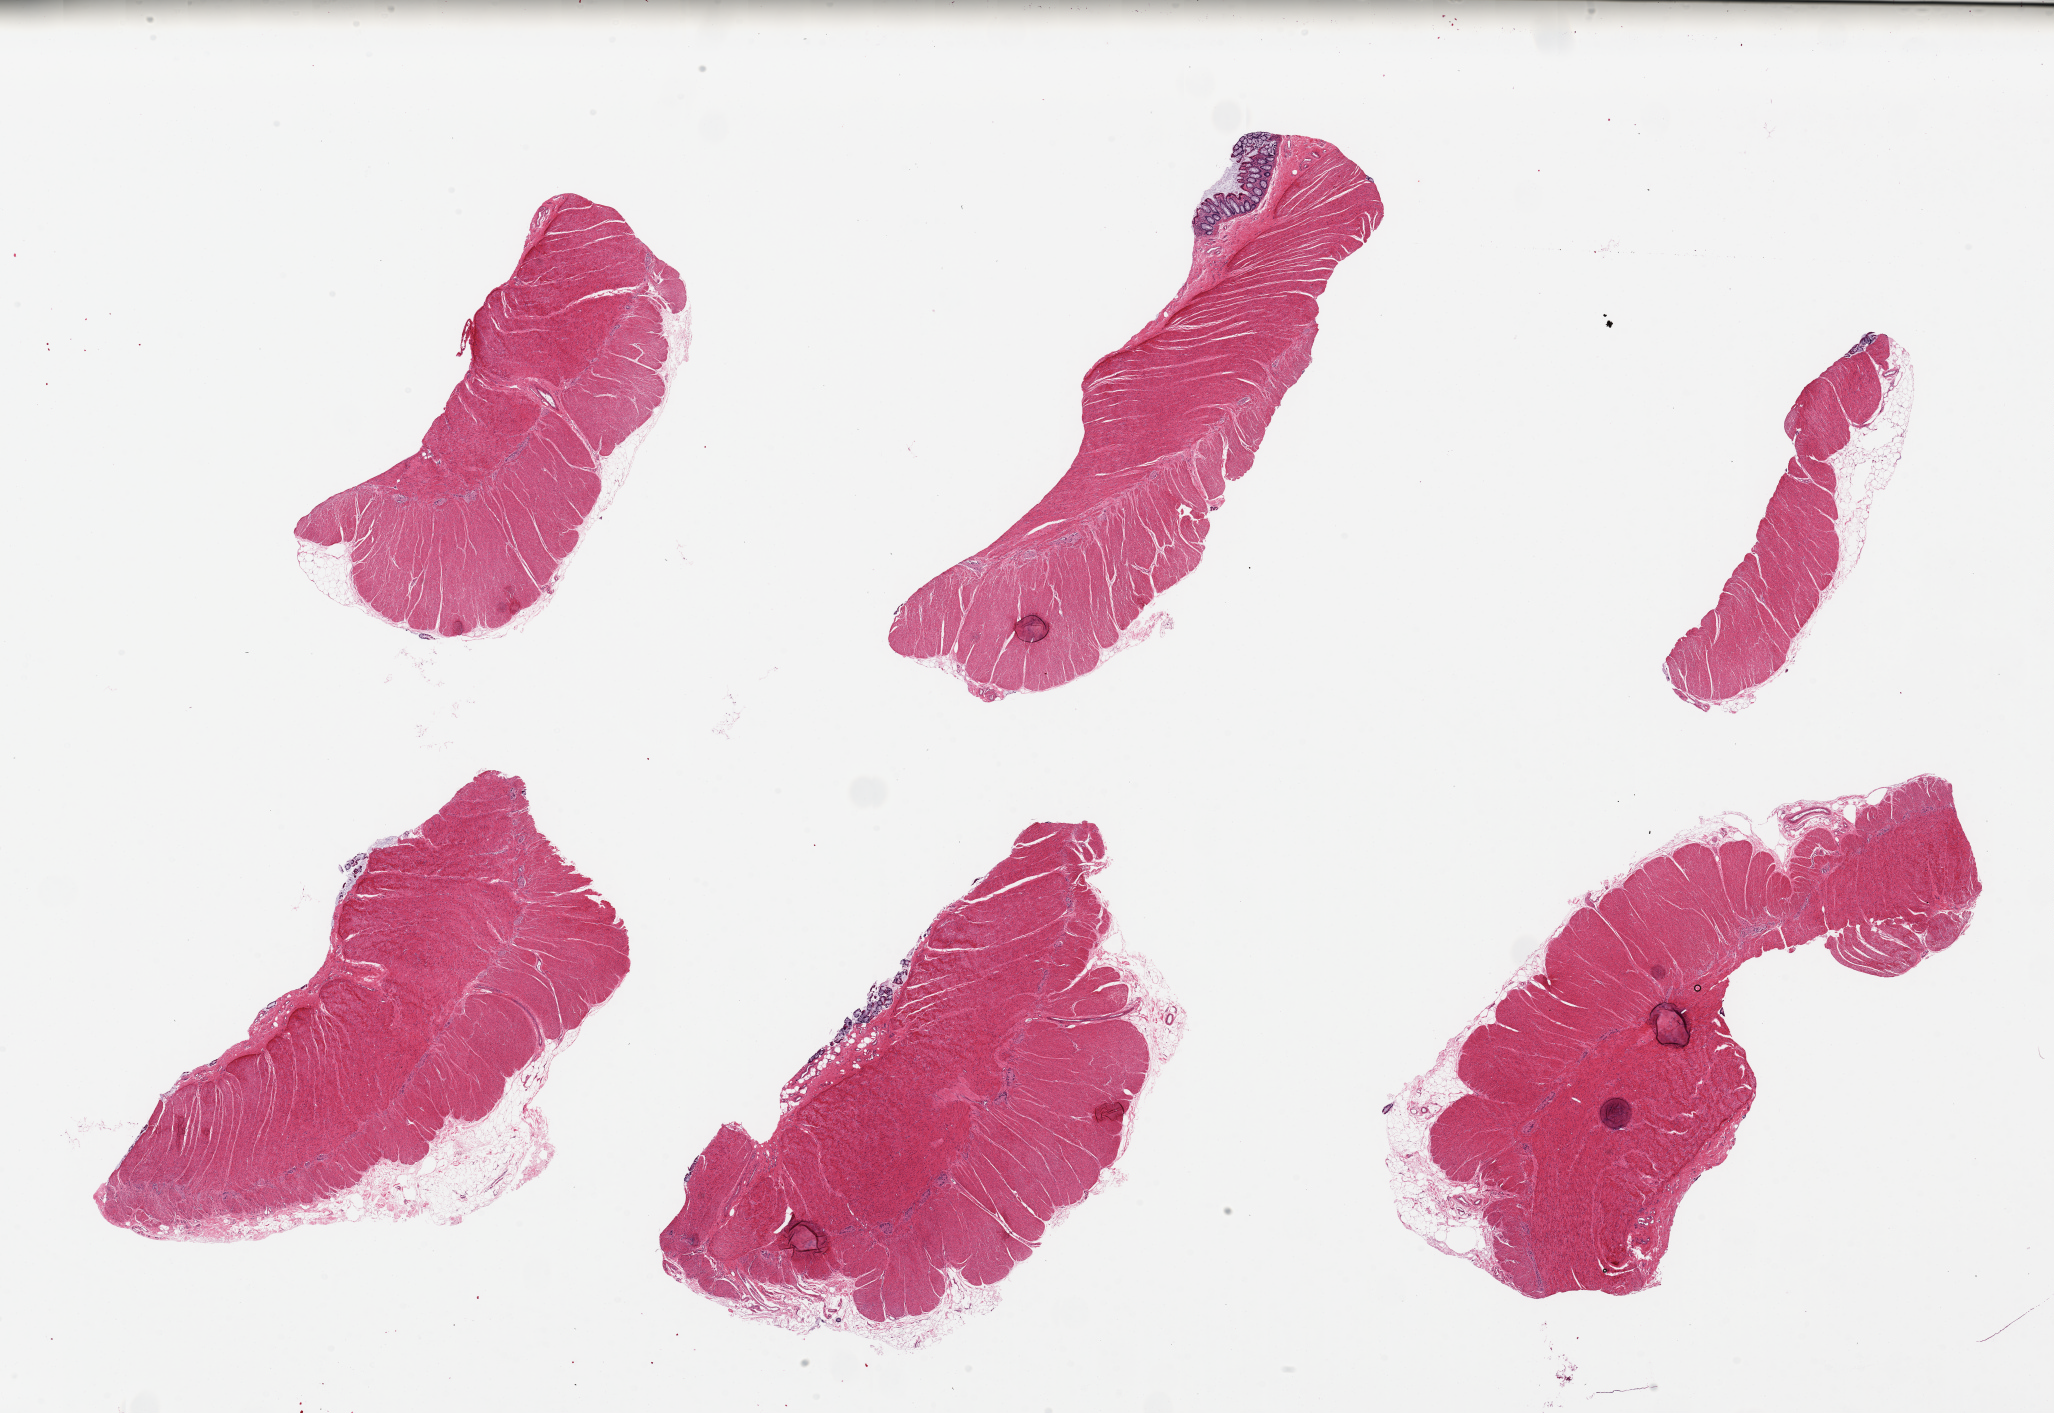
H&E whole-slide image, shown as a low-resolution overview of the whole scanned area (about 32.5 x 22.3 mm); PAXgene-fixed paraffin-embedded (PFPE) section; sampled site (target tissue): sigmoid colon; donor tissue sample. Donor sex: male.
• pathologist's review note for this sample: 6 pieces ~9x3mm, presumed sigmoid. Essentially all muscle, well preserved